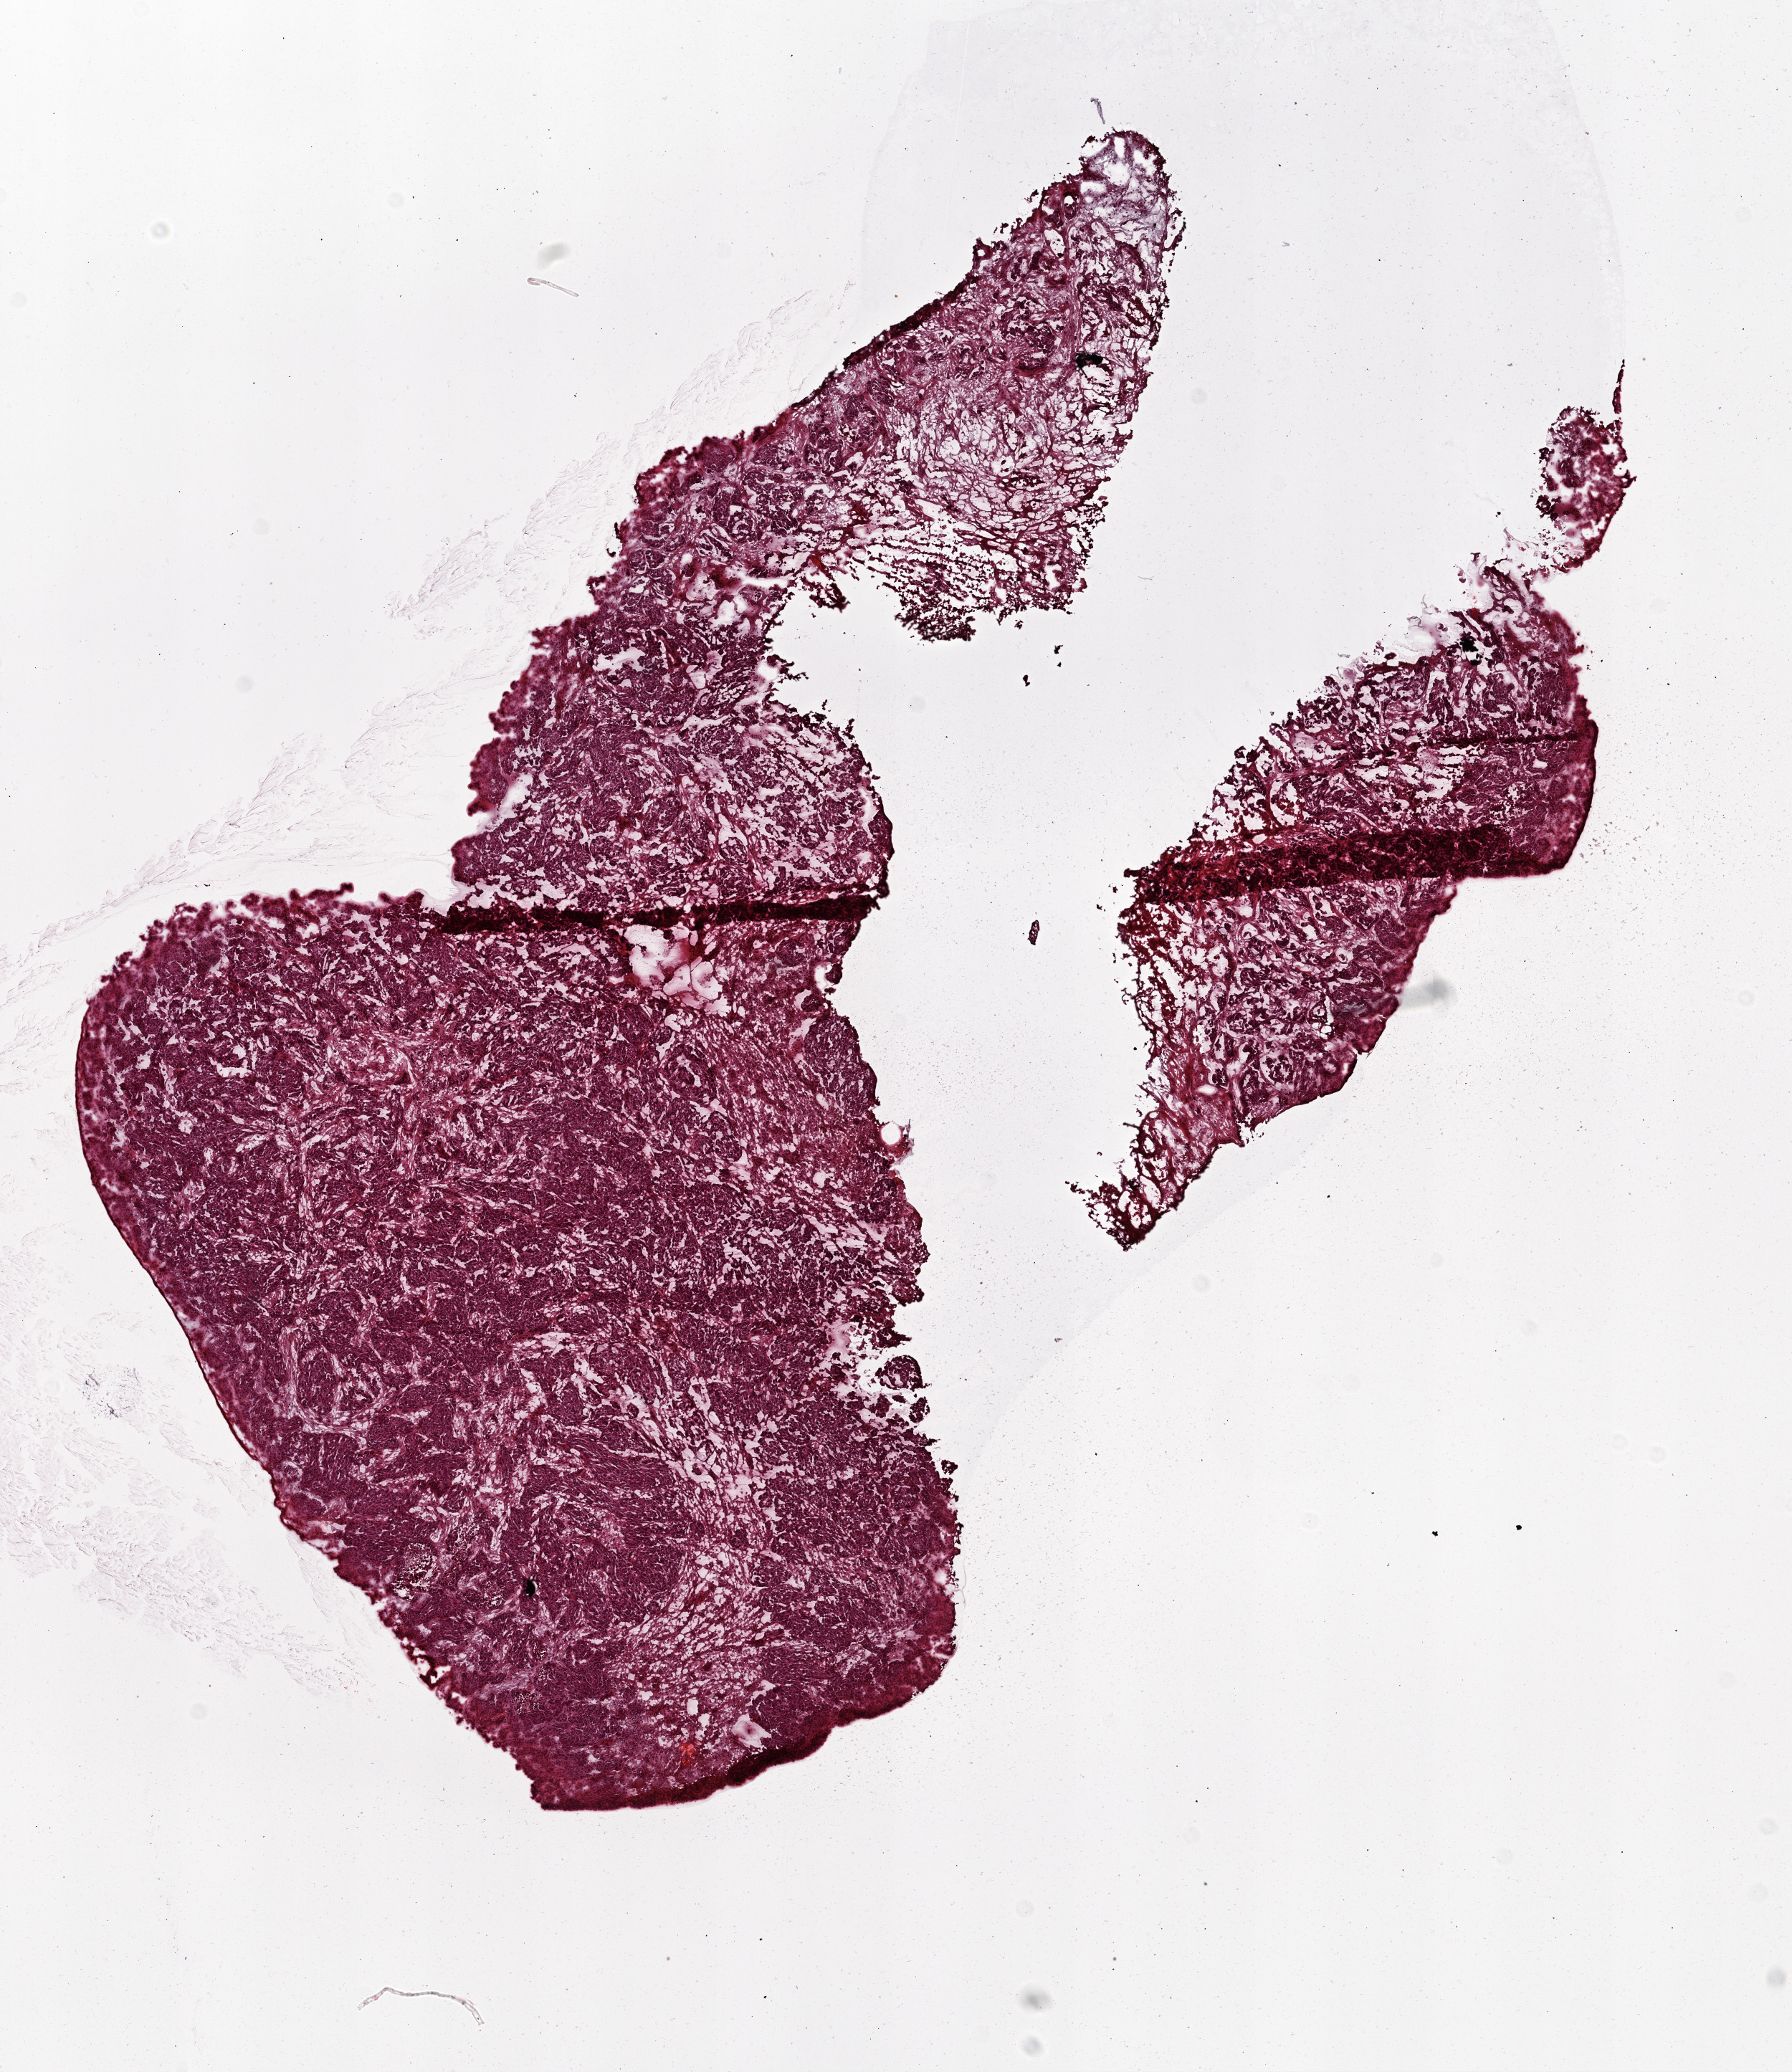
Digitized H&E-stained tissue section (whole slide) — shown as a low-resolution overview of the whole scanned area (about 10.0 x 11.6 mm, from a 20x scan). Frozen section from the top of the tissue portion. Ovary, primary tumour sample. Female patient; age at initial diagnosis 87 years. Histologic grade: G3 (poorly differentiated). Composition of this section per pathologist review: tumour cells 95%, tumour nuclei 85%, normal cells 0%, stromal cells 5%, necrosis 0%. Inflammatory infiltration, as recorded: lymphocyte infiltration 0%, monocyte infiltration 0%, neutrophil infiltration 0%.
Pathologic diagnosis: Serous cystadenocarcinoma, NOS. Laterality: bilateral. FIGO stage: IIIC.